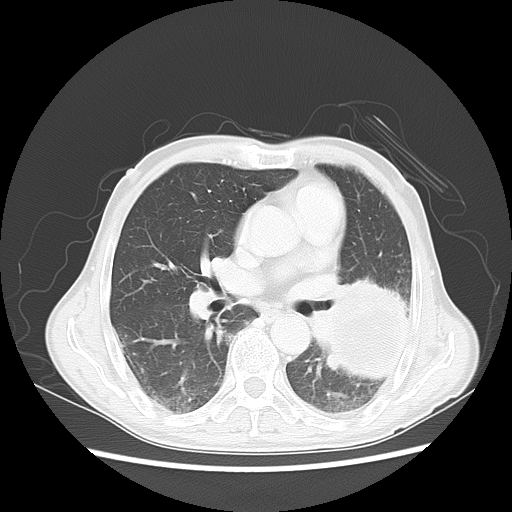
Chest CT, one axial slice. Position 27 of 51 along the scan axis. 120 kVp. Lung window (W 1500 / L -600 HU). 5 mm slice thickness. 512 × 512 image matrix, field of view 360 × 360 mm. Patient: male, 64 years. From the clinical record (not read from this slice): clinical TNM (as recorded): T4 N0 M0; histopathological grade: G2-3.
Annotated regions visible in this slice (rectangle marked by the reading radiologist):
- lung tumour (recorded histology: squamous cell carcinoma): bounding box (x1, y1, x2, y2) in pixels: (310, 268, 422, 387)